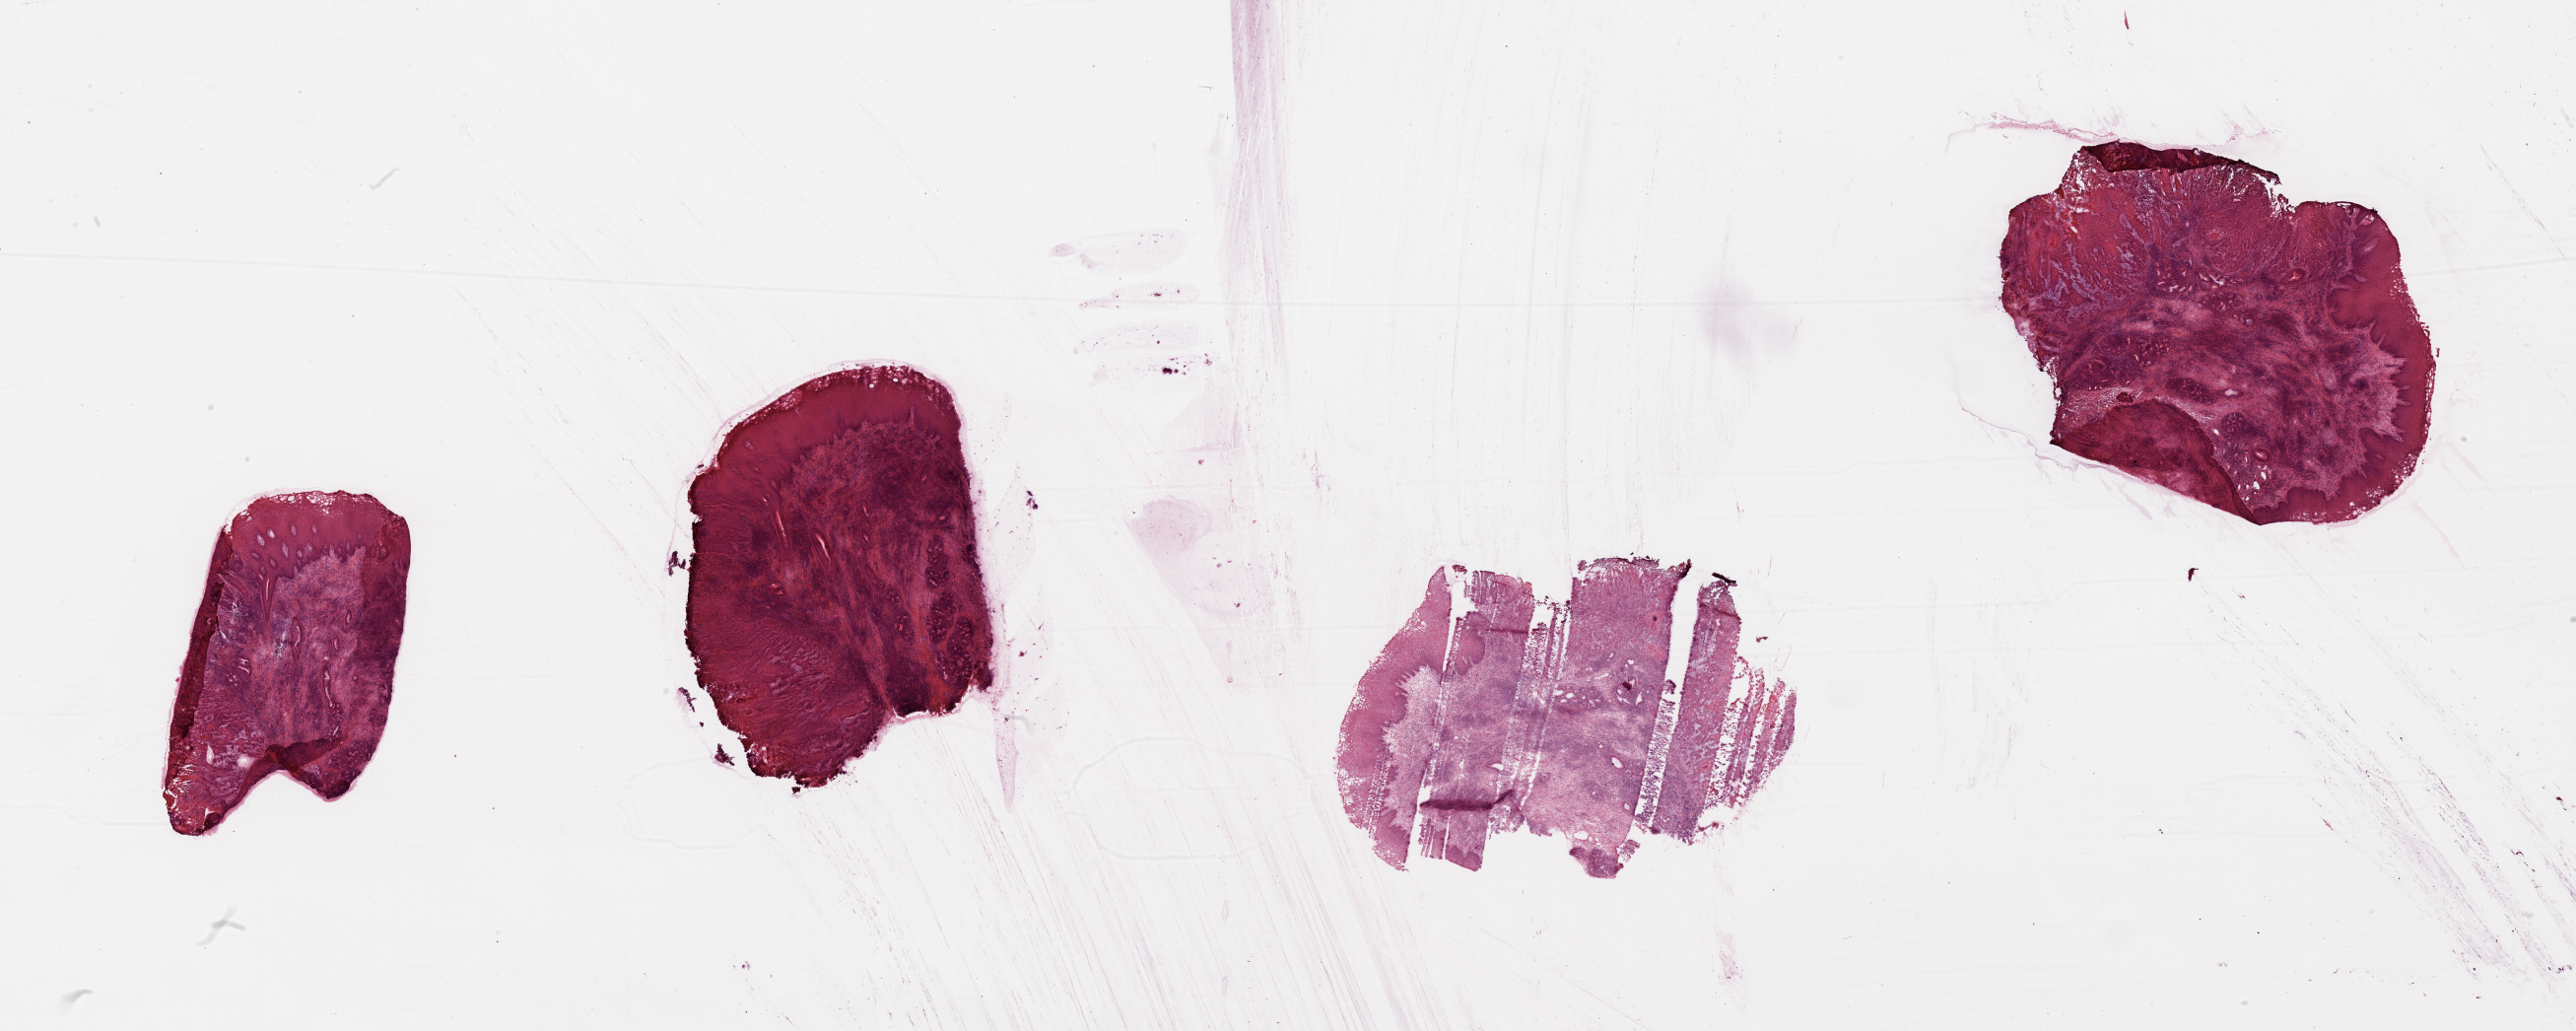
Digitized H&E tissue section (whole slide), a low-resolution overview of the entire scanned area, about 41.3 x 16.5 mm (acquisition: 20x scan); tumour tissue sample, sampled site: larynx. Female, 54 y/o. Histologic grade: G2 (moderately differentiated). Slide review estimates, as recorded: tumour nuclei 60%, necrosis 5%.
* histologic diagnosis: Squamous cell carcinoma, NOS
* AJCC pathologic stage: III